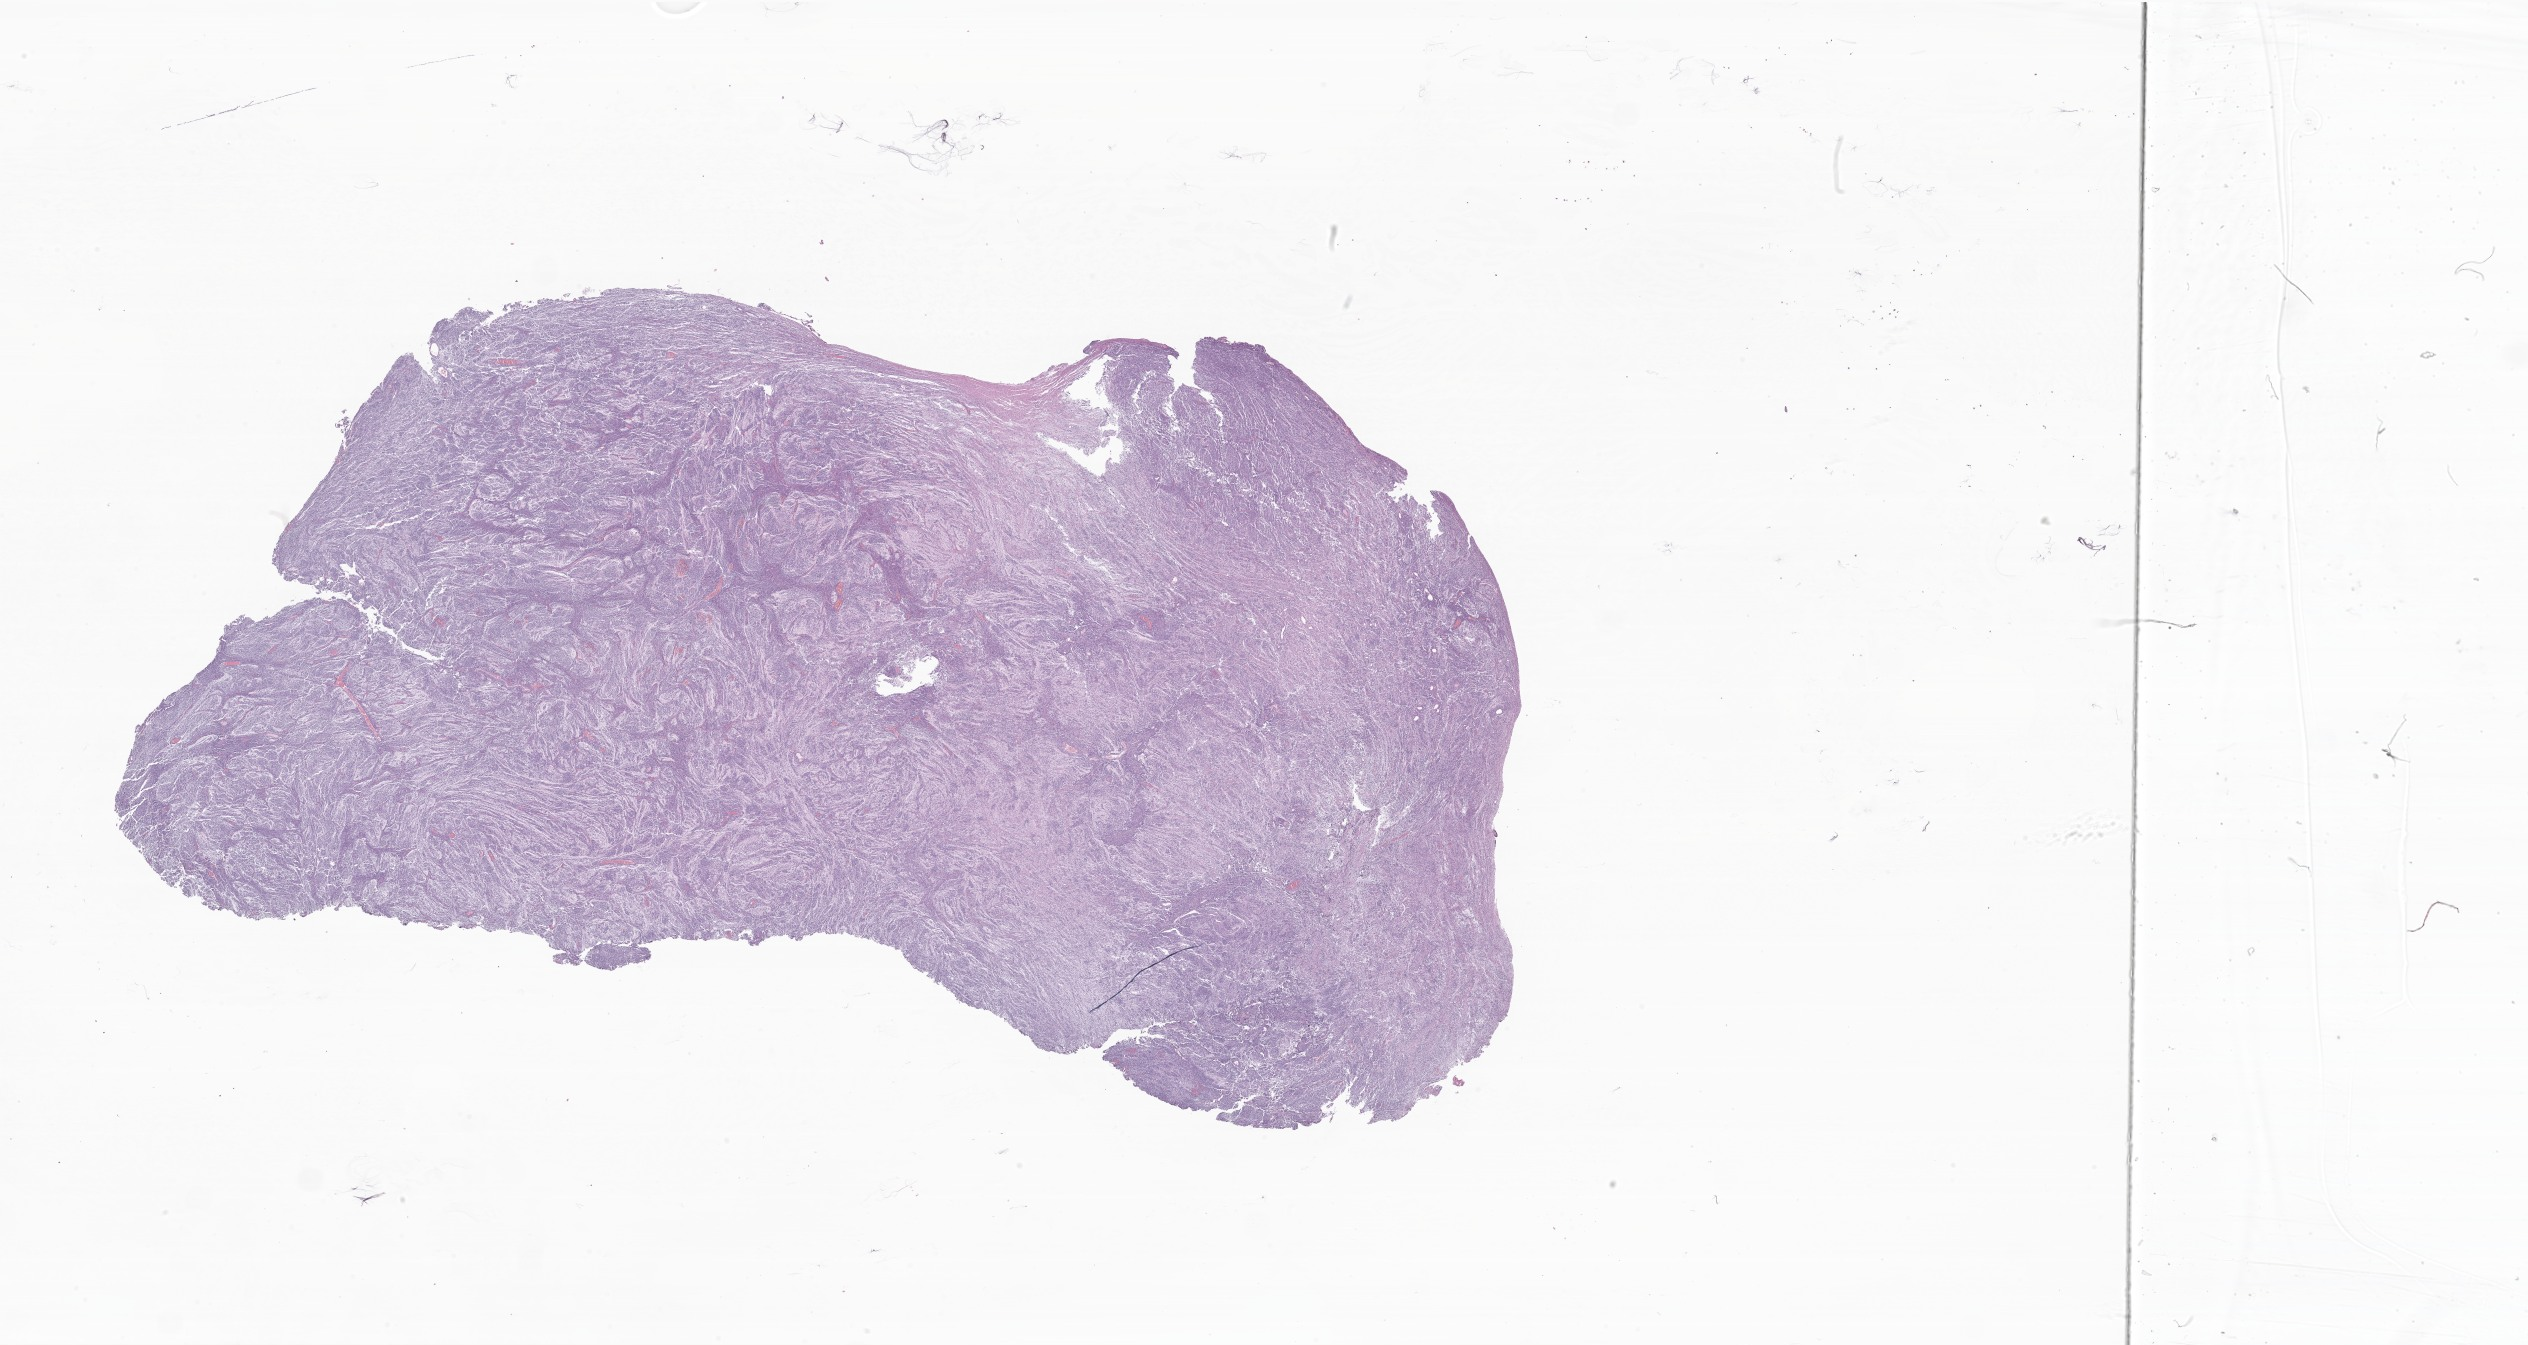
Whole-slide image, H&E stain of tumor tissue from the cerebellum, low-resolution overview of the scanned area, about 42.6 x 22.7 mm; formalin-fixed, paraffin-embedded (FFPE) tissue. Patient male; age 38 months.
Diagnosis (ICD-O-3 morphology term): Medulloblastoma, NOS.